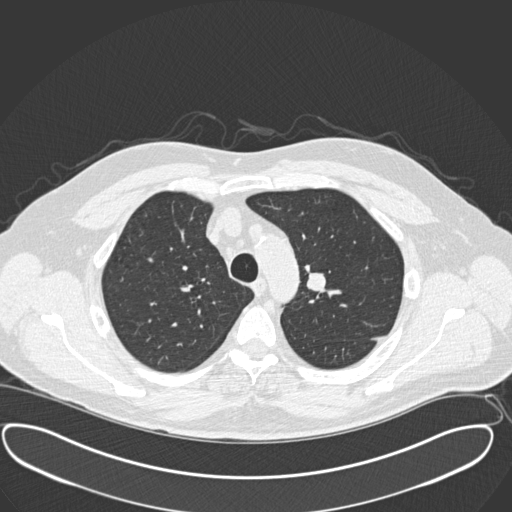
Chest CT (low-dose screening protocol), one axial image; third screening round (two years after baseline); lung window (W 1500 / L -600 HU); 2 mm slice thickness; slice 45 of 181 in the series; 512 × 512 image matrix. Male, age 56 years at enrolment.
- Expert reader's lesion annotation, bounding box [x1, y1, x2, y2] px = [289, 262, 343, 309].
- No non-calcified nodule or mass ≥4 mm was recorded by the screening reader at this exam.
- Later outcome: lung cancer diagnosed 156 days after this screen — neuroendocrine carcinoma, NOS, left upper lobe, well differentiated (G1), stage IA (AJCC 6th edition), 20 mm at pathology.